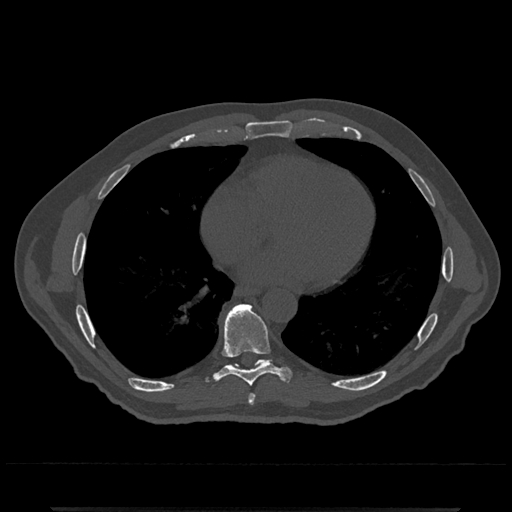
CT including the spine, one axial slice. Position 664 of 797 along the scan axis. Reconstruction kernel Br40s/3. 120 kVp. Bone window (W 1800 / L 400 HU). 0.5 mm slice thickness. 512 × 512 image matrix. Patient: male, 67 years. Case-level facts recorded for this patient, not image findings: primary cancer: prostate.
Outlined on this slice (semi-automatically segmented with operator editing):
- T7 vertebra: bounding box <248,394,255,404> (left, top, right, bottom; pixels)
- T8 vertebra: <214,304,290,387>
- T9 vertebra: <226,365,234,367>